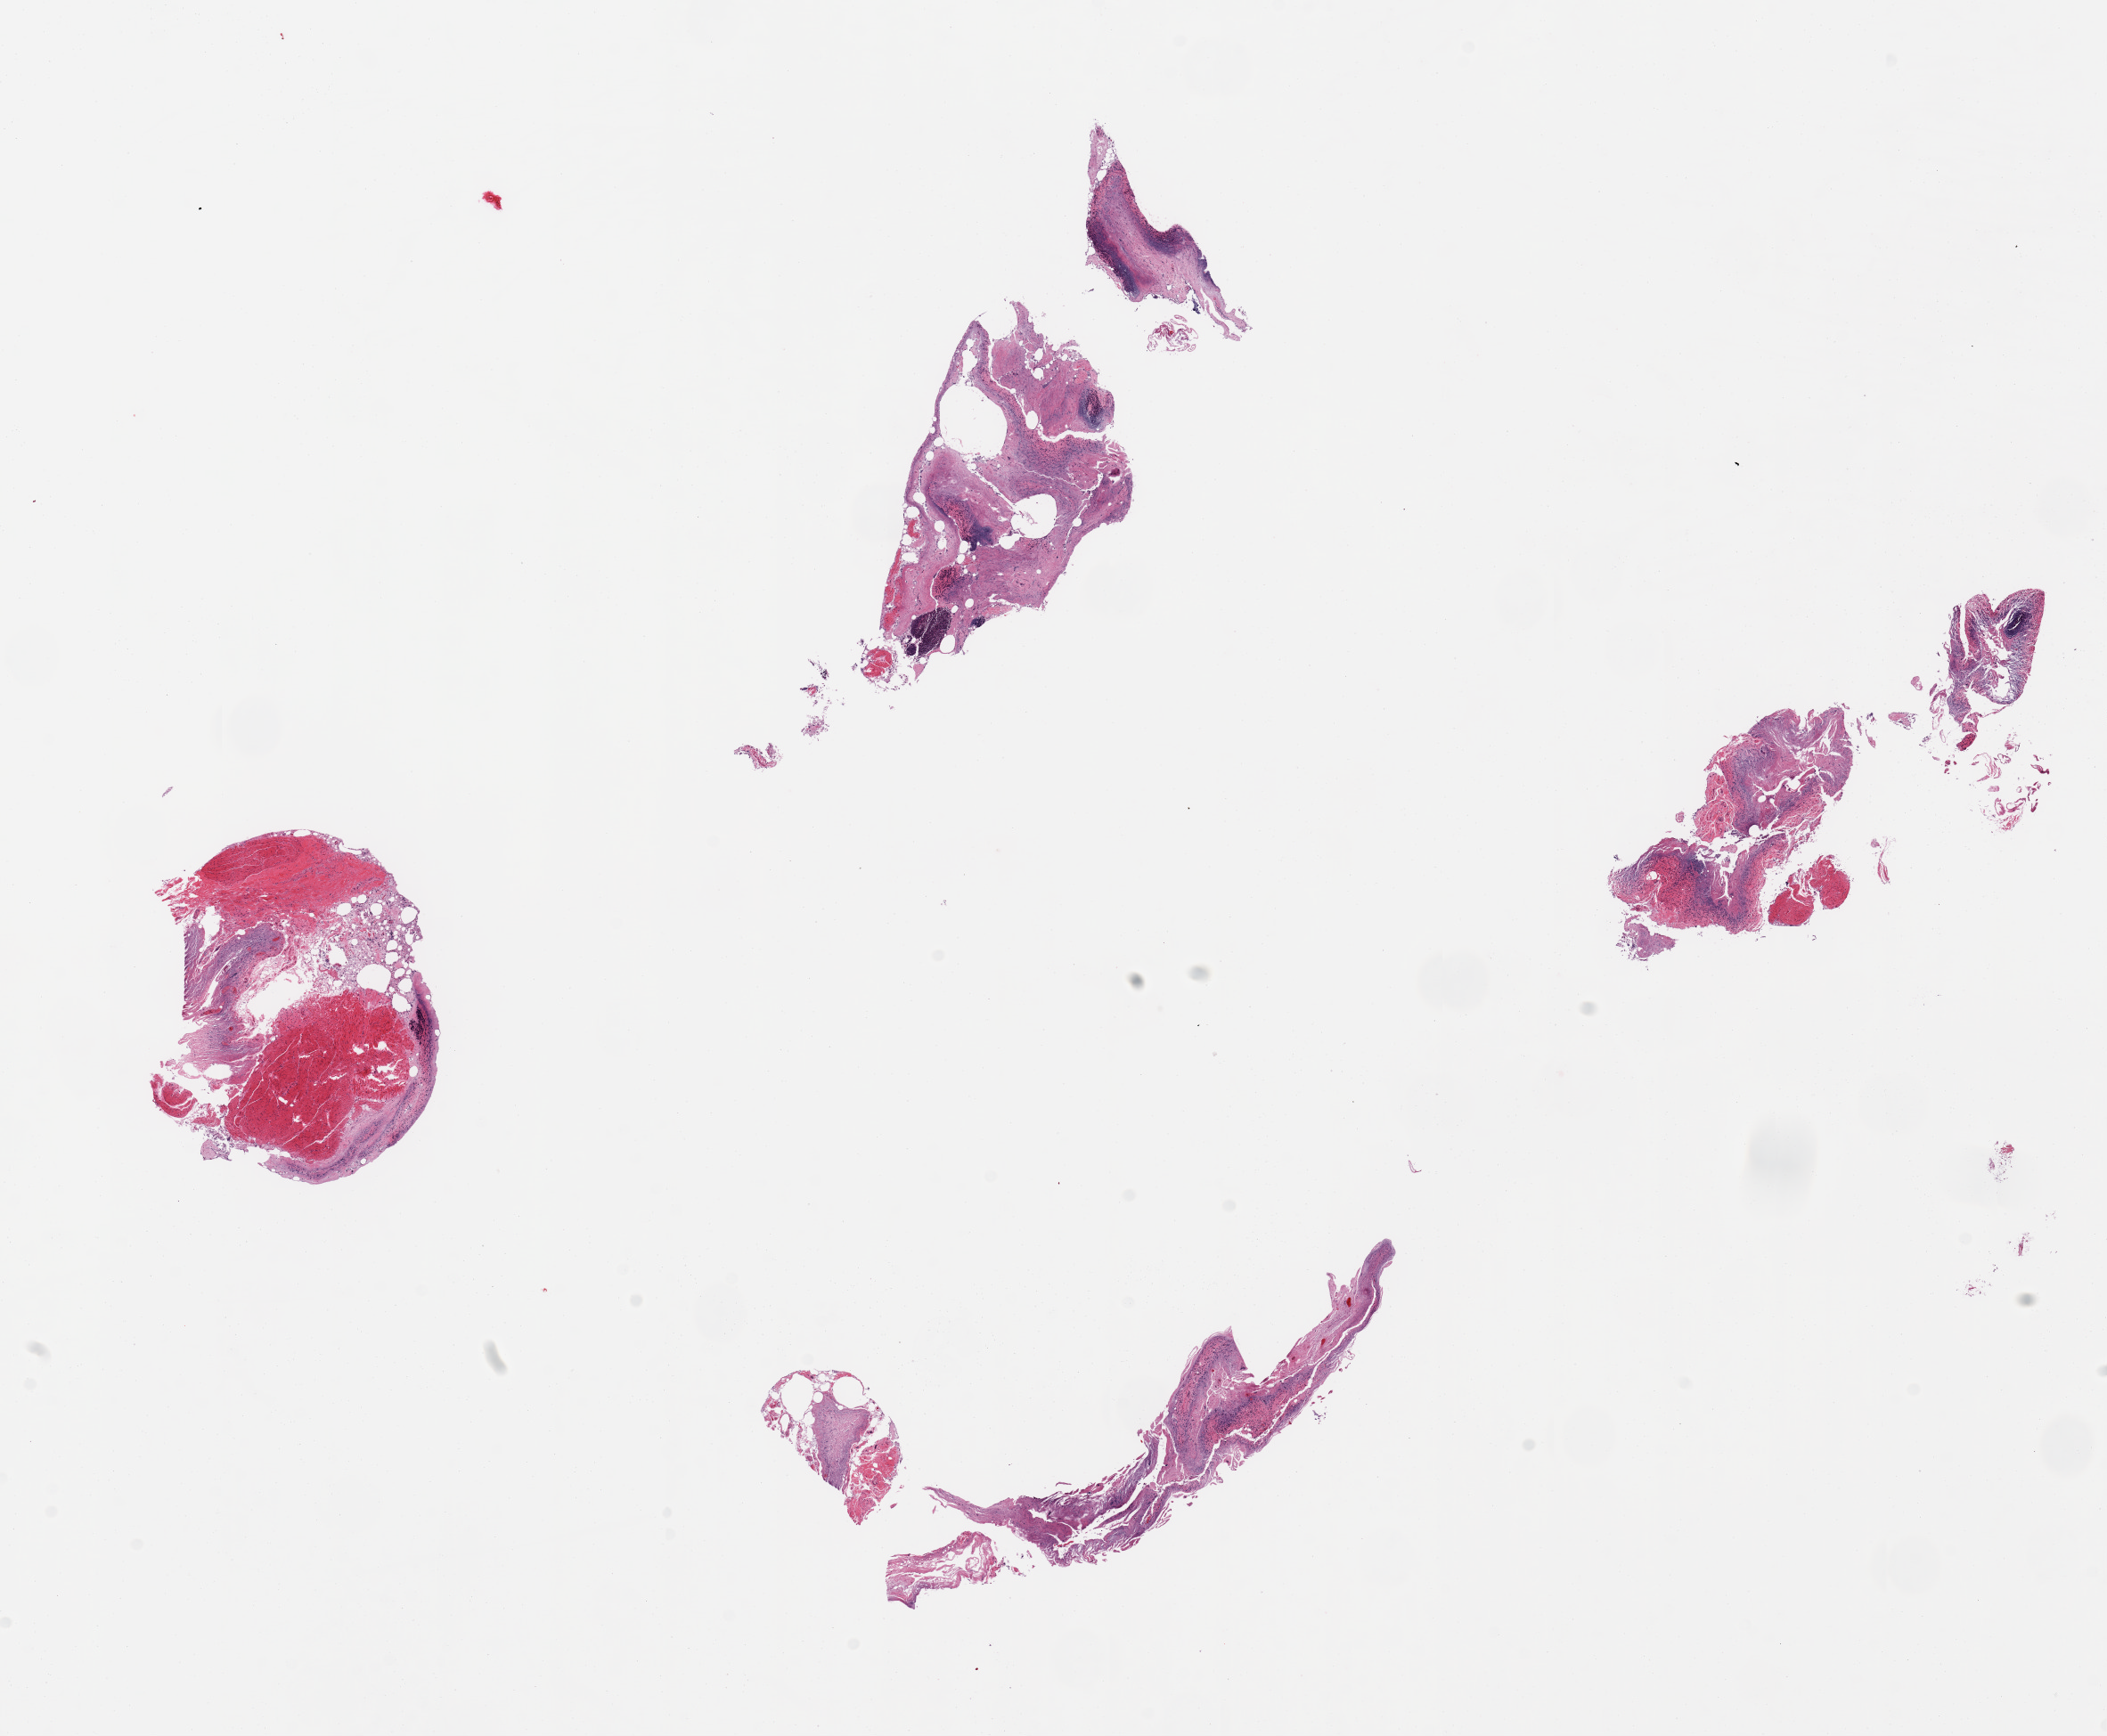
H&E whole-slide image — a low-resolution overview of the entire scanned area, about 18.7 x 15.4 mm (from a 20x scan). PAXgene-fixed paraffin-embedded (PFPE) section. Sampled site (target tissue): ileum. Tissue donor sample. Male donor.
Review note (as recorded): 4 pieces, muscularis and severely autolyzed mucosa, small focus of residual lymphoid tissue.